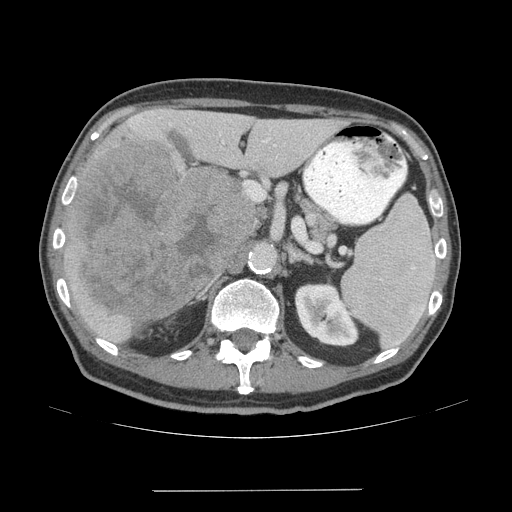
Contrast-enhanced abdominal CT (liver protocol), one axial slice. Position 32 of 77 along the scan axis. 140 kVp. Soft-tissue window (W 400 / L 40 HU). 512 × 512 image matrix, field of view 400 × 400 mm. From the clinical record (not read from this slice): diagnosis: hepatocellular carcinoma (patient treated with transarterial chemoembolisation; whether this scan precedes or follows treatment is not stated here); TNM stage (as recorded): Stage-IVA; Child-Pugh class: A; tumour differentiation: well differentiated; tumour nodularity: uninodular.
Structures marked on this image (semi-automatically segmented with operator editing):
- liver parenchyma outside the tumour (the mass and vessels are separate outlines, so this box may not span the whole liver): box from (x=64, y=108) to (x=347, y=344) px
- mass: (x=67, y=138)–(x=255, y=318)
- liver vessels: (x=244, y=140)–(x=276, y=186)